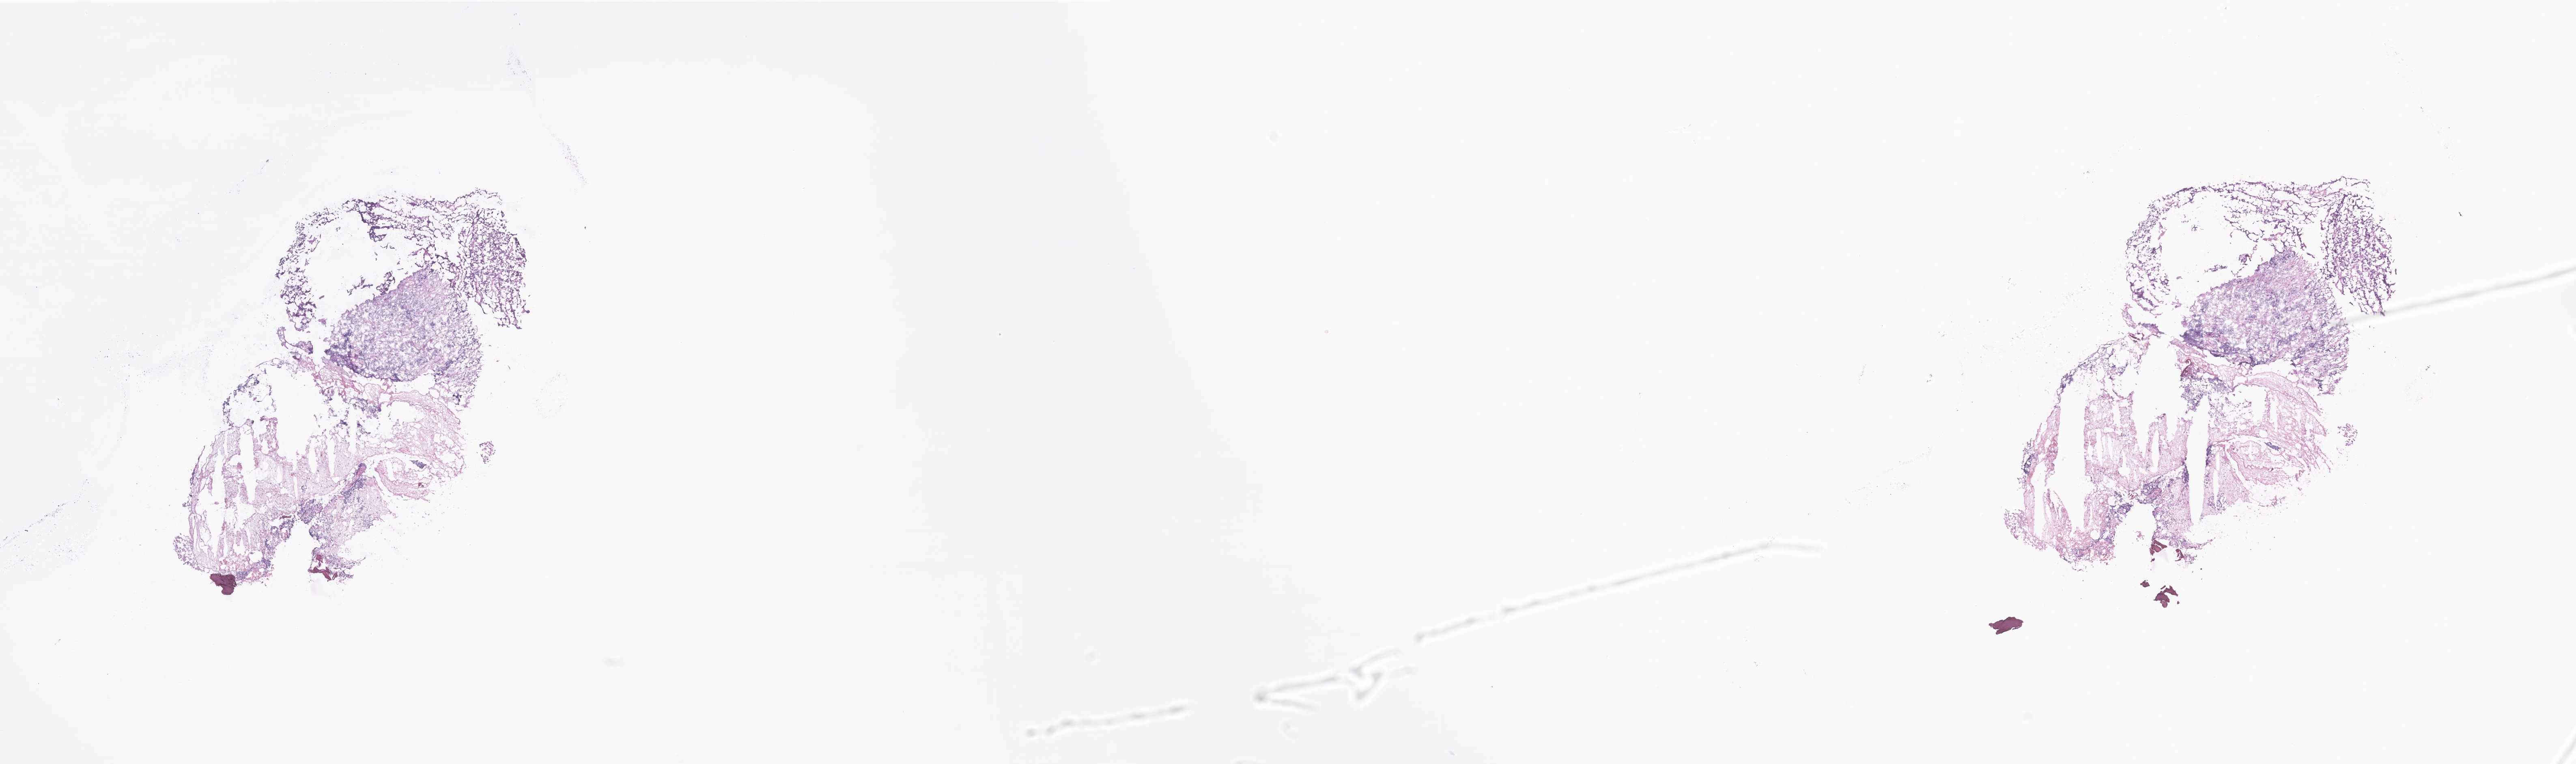
Digitized haematoxylin and eosin-stained section of tumor tissue from the abdomen, shown as a low-resolution overview of the whole scanned area (about 26.8 x 7.9 mm). Female patient, age 215 months (17 years 11 months).
- specimen: frozen section